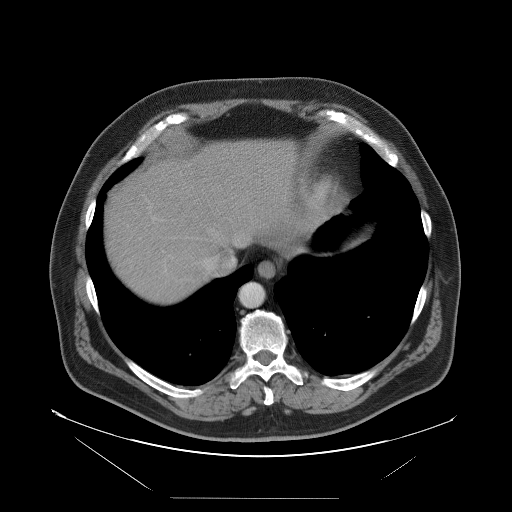
Contrast-enhanced abdominal CT, one axial slice; slice 87 of 114 in the series (ordered by position); intravenous contrast given; soft-tissue window (W 400 / L 40 HU); 512 × 512 image matrix, field of view 500 × 500 mm. Male patient, age 61 years. From the clinical record (not read from this slice): diagnosis: colorectal cancer liver metastases, imaged before liver resection; multiple liver metastases: no; largest metastasis: 6.5 cm; disease in both lobes: yes.
Structures marked on this image (manually delineated by an expert):
- hepatic veins: bounding box <201,229,240,272> (left, top, right, bottom; pixels)
- liver: <106,140,298,303>
- planned liver remnant (the part of the liver to remain after resection): <158,141,300,255>